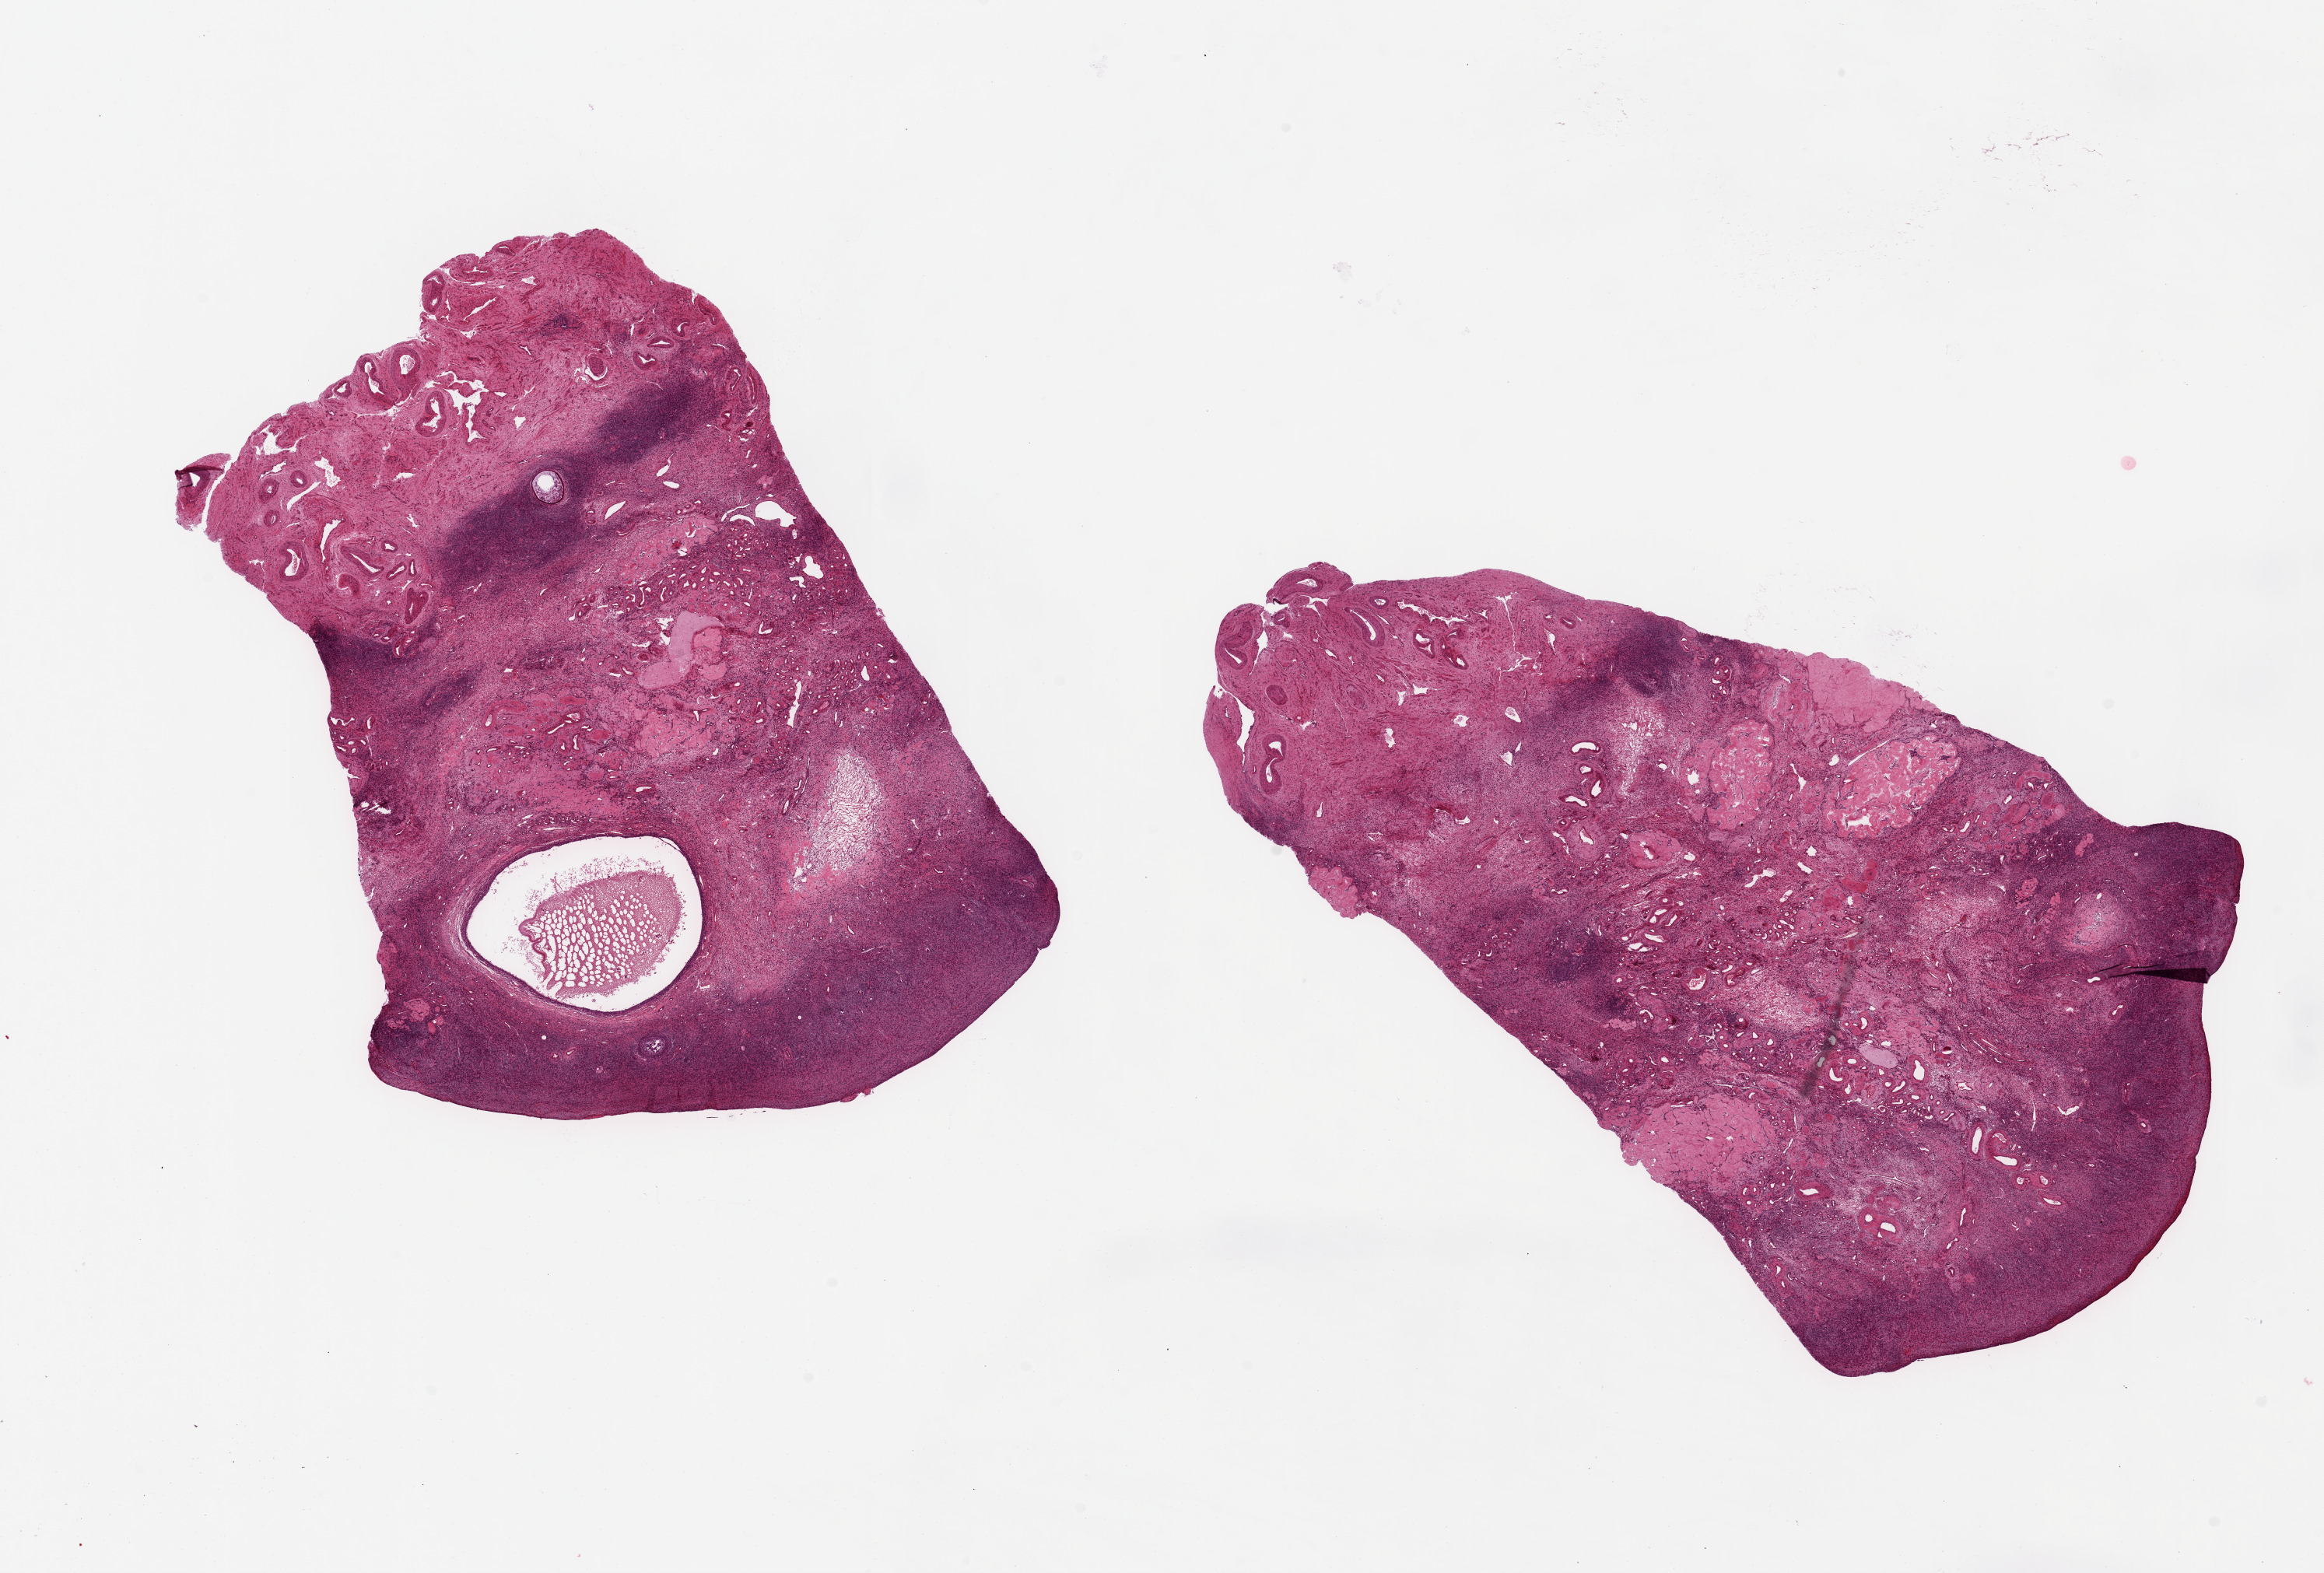
Hematoxylin and eosin (H&E) whole-slide image — low-resolution overview of the scanned area, about 23.6 x 16.0 mm, PAXgene-fixed paraffin-embedded (PFPE) section, target tissue: ovary, tissue donor sample. Donor sex: female.
Pathologist's review note for this sample: 2 pieces, 9x7 & 11x7mm; ova and follicles present.